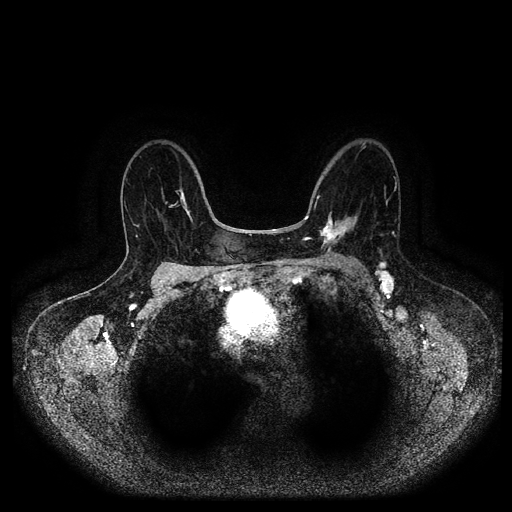
Breast MRI (dynamic contrast-enhanced, multi-phase), one axial slice; position 61 of 116 along the scan axis; dynamic contrast-enhanced series, time point 2 of 5 at this slice position (early post-contrast); 1.5 T; TE 2.6 ms, TR 5.2 ms; 2 mm slice thickness; 512 × 512 image matrix. Patient: female, 69 years.
Outlined on this slice (semi-automatically segmented with operator editing):
- breast lesion (labelled 'tumour' in the annotation; benign lesions carry a separate 'benign' label): bounding box (x1, y1, x2, y2) in pixels: (319, 211, 359, 251)